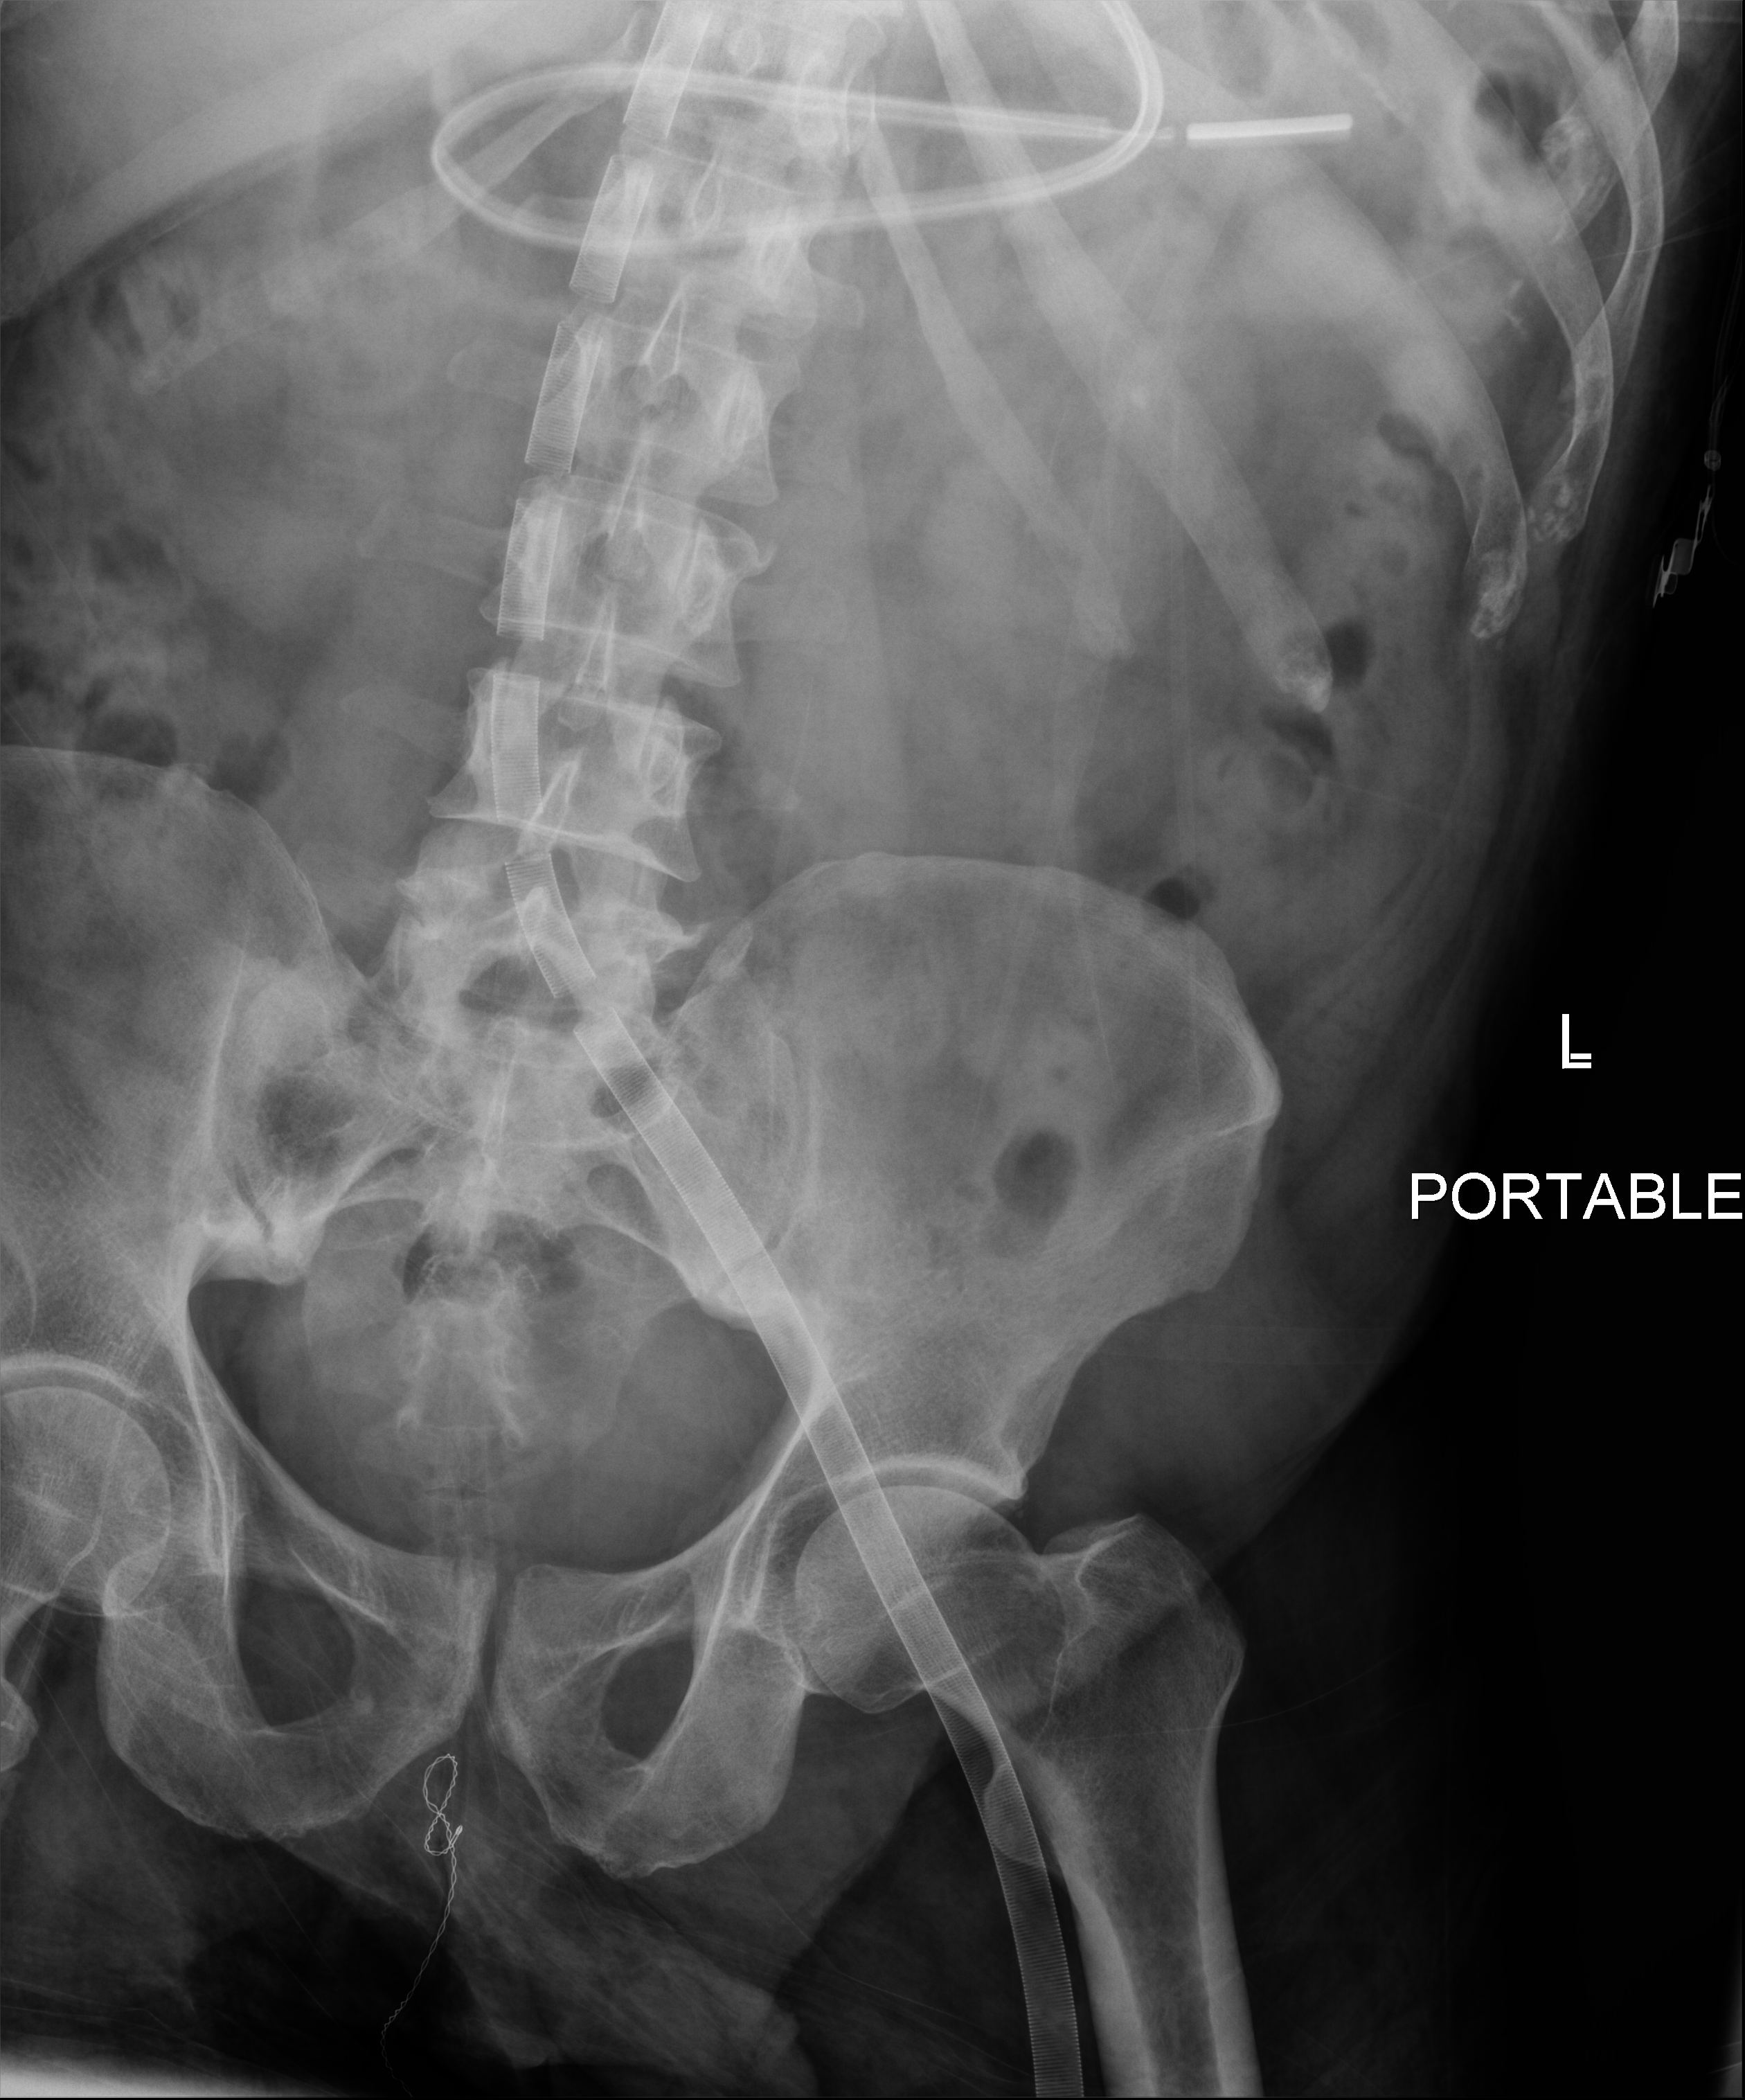
Bedside abdomen radiograph (digital radiography), anteroposterior (AP) projection. Patient hospitalised with COVID-19; male, aged 18–59 years.
Admission-level facts for this patient (not findings on this image; timing relative to this image not recorded): admitted to intensive care during this hospital stay: yes.